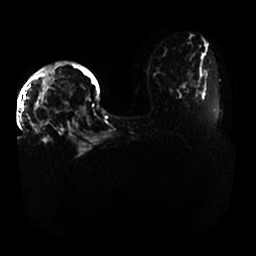
Breast MRI, one axial slice; position 17 of 33 along the scan axis; diffusion-weighted series; image 2 of 4 stored at this slice position (different b-values; order by instance number); 1.5 T; 256 × 256 image matrix. Female patient.
Annotated regions visible in this slice (expert manual segmentation):
- tumour on diffusion-weighted imaging: bounding box <34,95,44,120> (left, top, right, bottom; pixels)